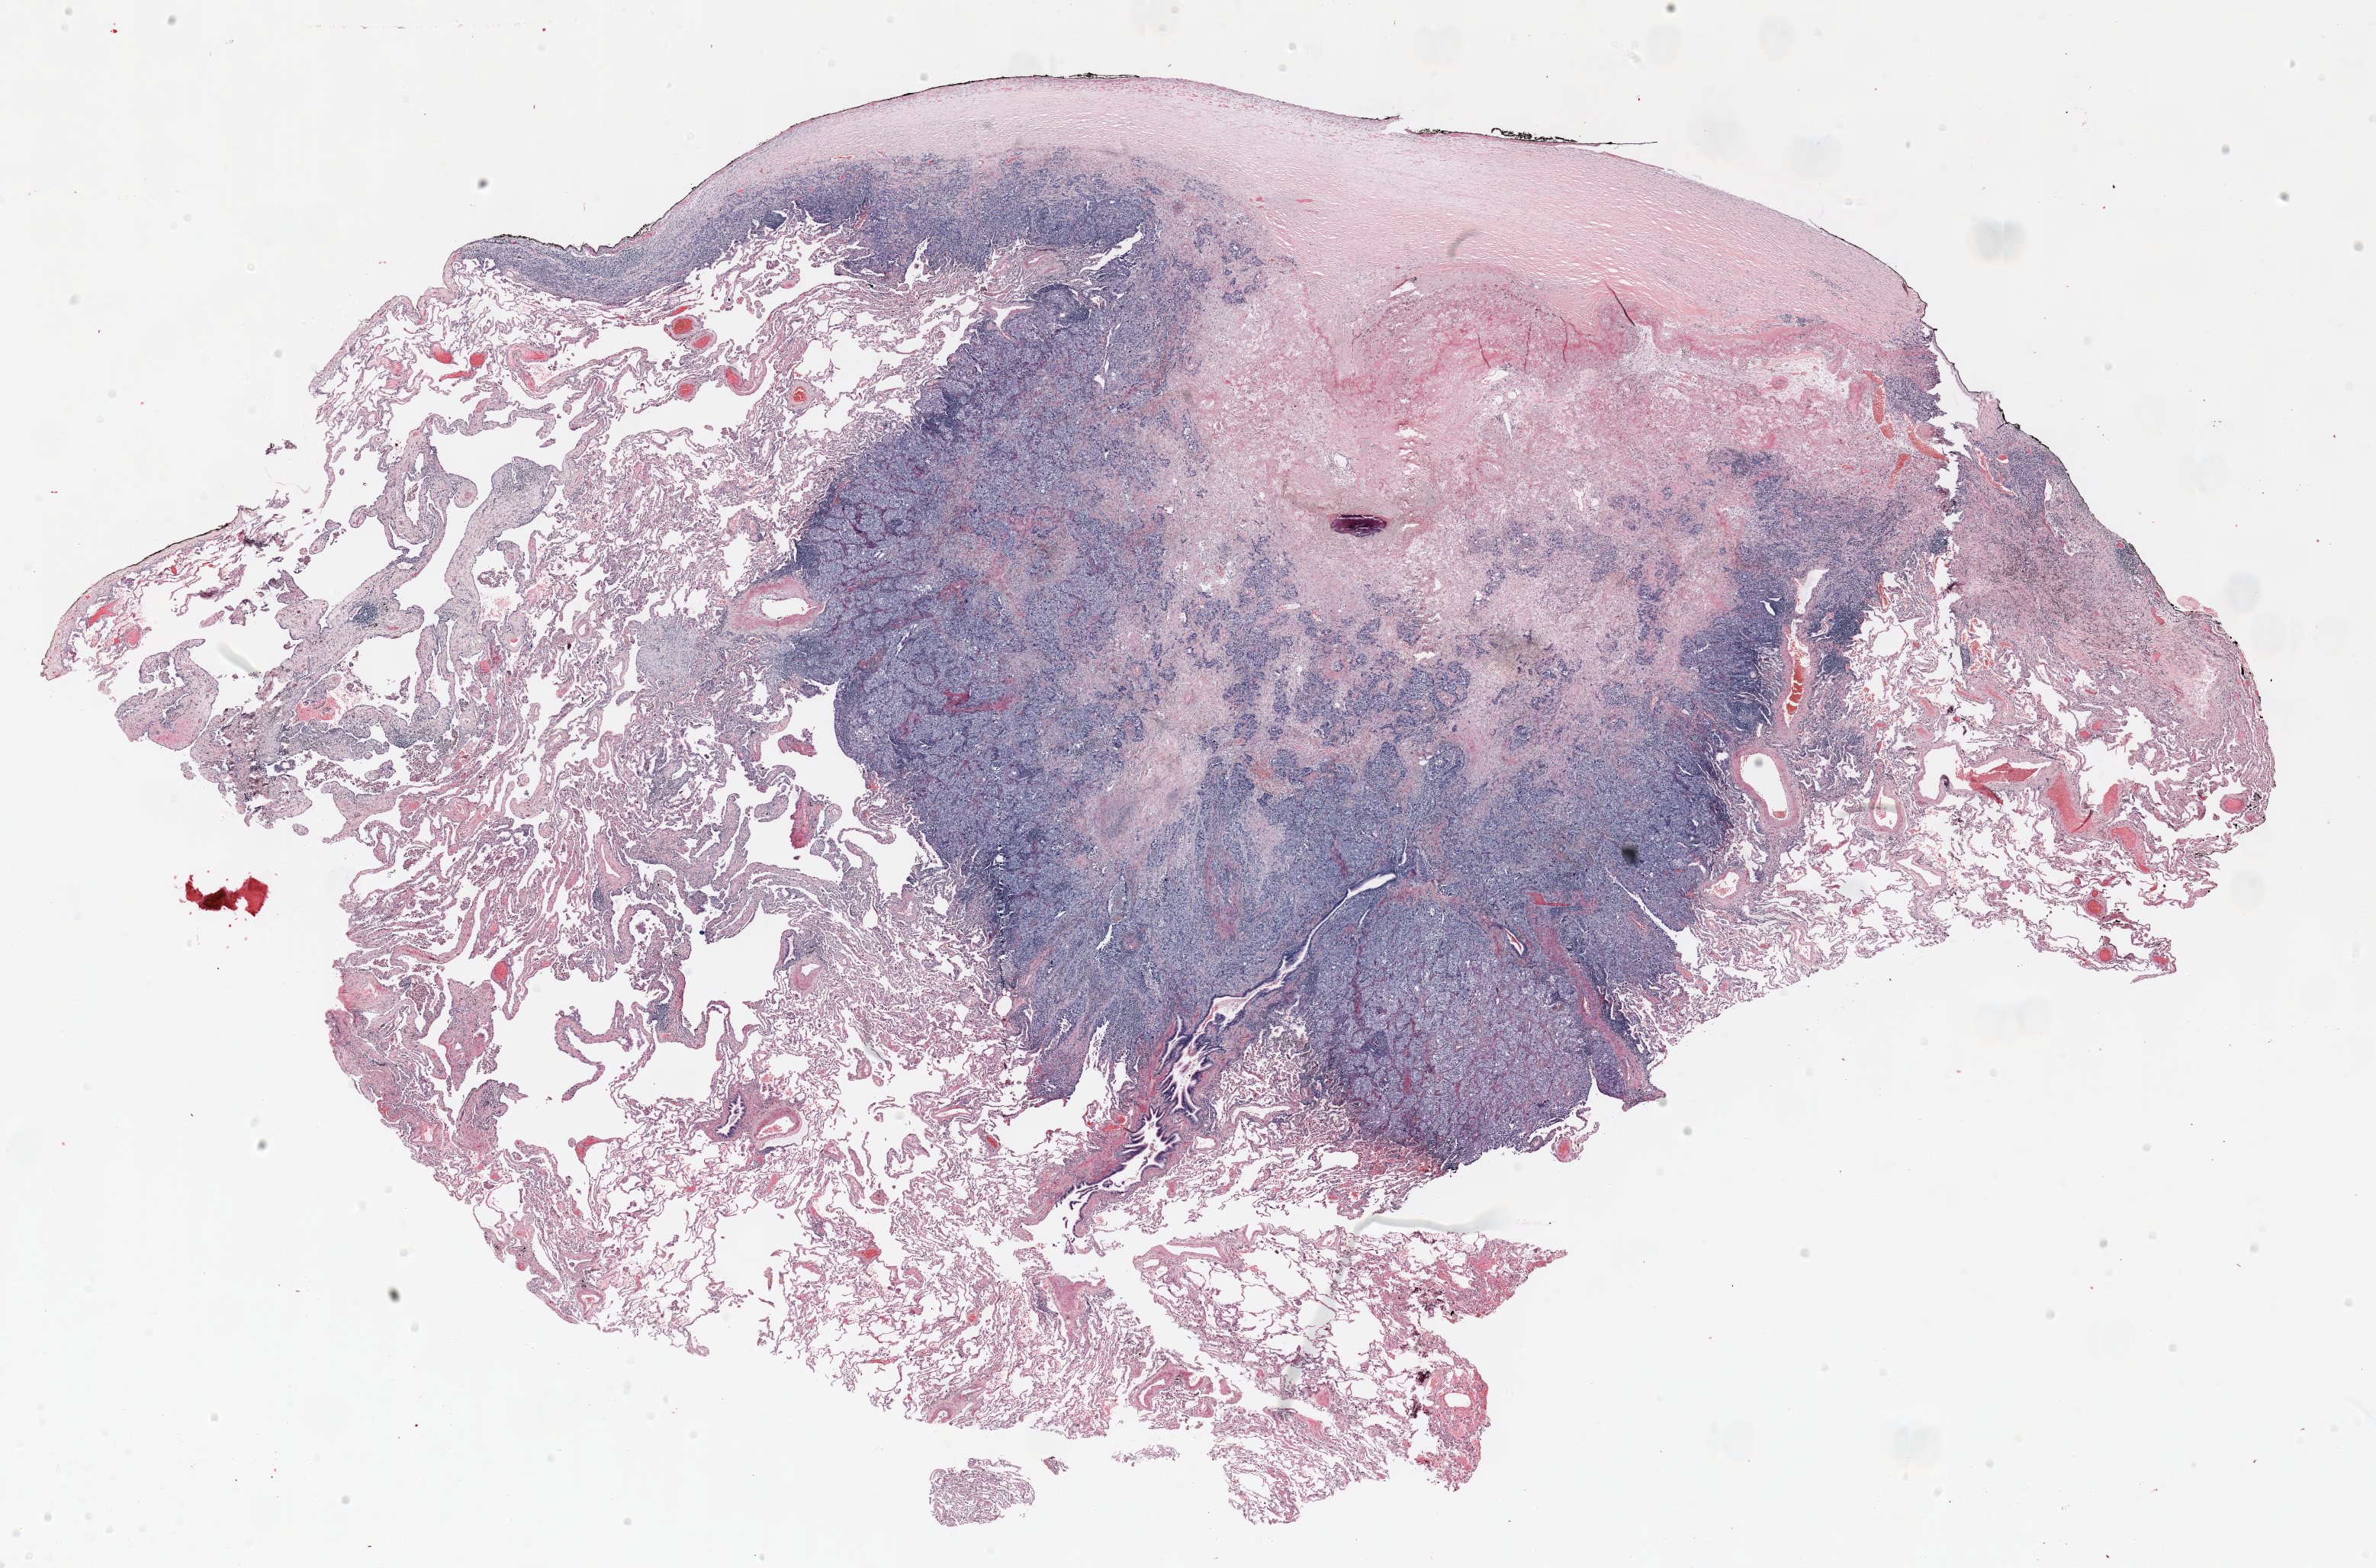
H&E whole-slide image, shown as a low-resolution overview of the whole scanned area (about 25.0 x 16.5 mm, slide scanned at 20x), formalin-fixed paraffin-embedded (FFPE) section, lung. Female patient, aged 56 at enrolment. Current smoker at enrolment. Grade: poorly differentiated (G3).
Tumour size (pathology): 15 mm. Participant's lung-cancer diagnosis: Large cell carcinoma, NOS (ICD-O-3 8012/3). Stage (AJCC 6th edition): IB. Primary tumour location (clinical record): right upper lobe.